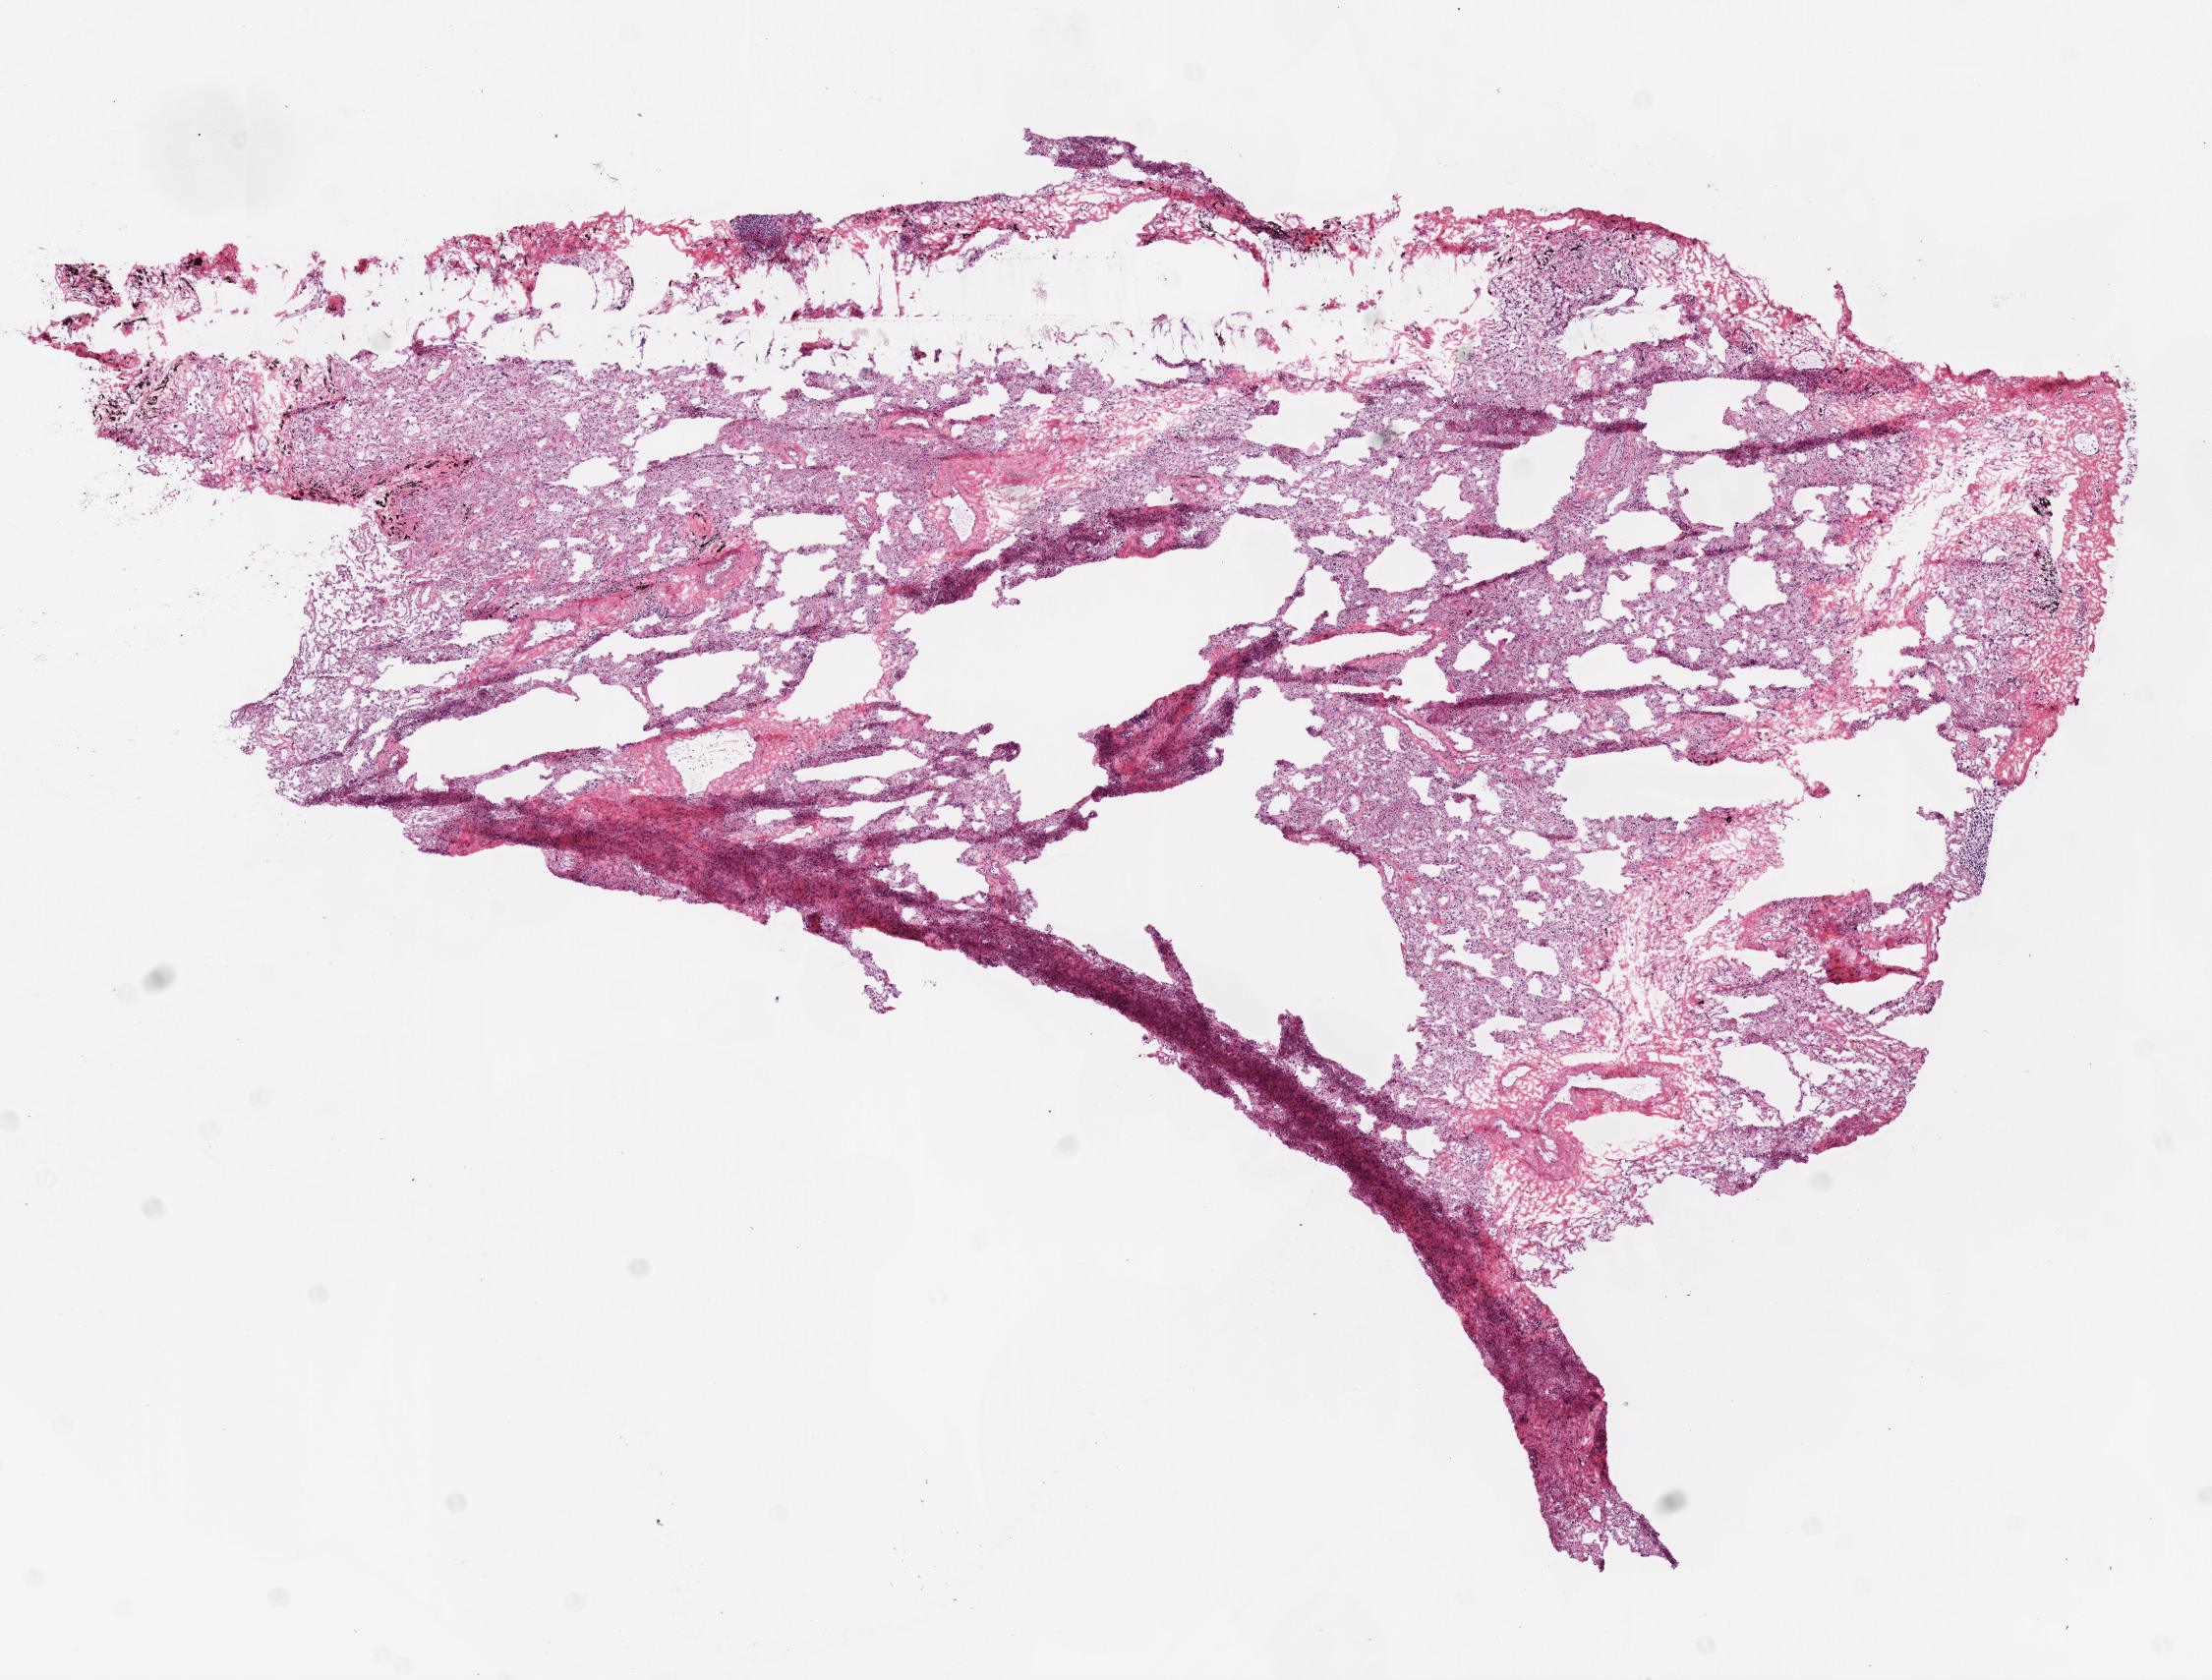
Digitized Hematoxylin and eosin (H&E) stained tissue section (whole slide), shown as a low-resolution overview of the whole scanned area (about 9.0 x 6.9 mm), frozen section, lung, solid tissue normal (non-tumour tissue) sample. Male patient; age at initial diagnosis 70 years.
This section: solid tissue normal sample (biorepository sample class). Patient diagnosis: Squamous cell carcinoma, NOS.